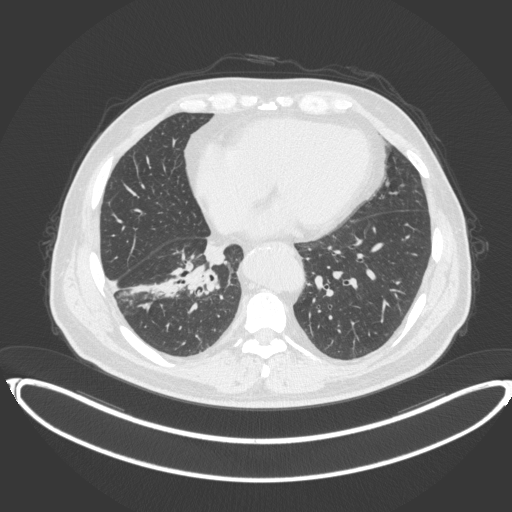
Chest CT, one axial slice. Slice 148 of 383 in the series (ordered by position). Reconstruction kernel B31f. 120 kVp. Lung window (W 1500 / L -600 HU). 512 × 512 image matrix, field of view 448 × 448 mm. Male patient, age 61 years. Case-level facts recorded for this patient, not image findings: clinical TNM (as recorded): T1b N1 M0.
Structures marked on this image (rectangle marked by the reading radiologist):
- lung tumour (recorded histology: squamous cell carcinoma): bounding box <182,264,220,298> (left, top, right, bottom; pixels)